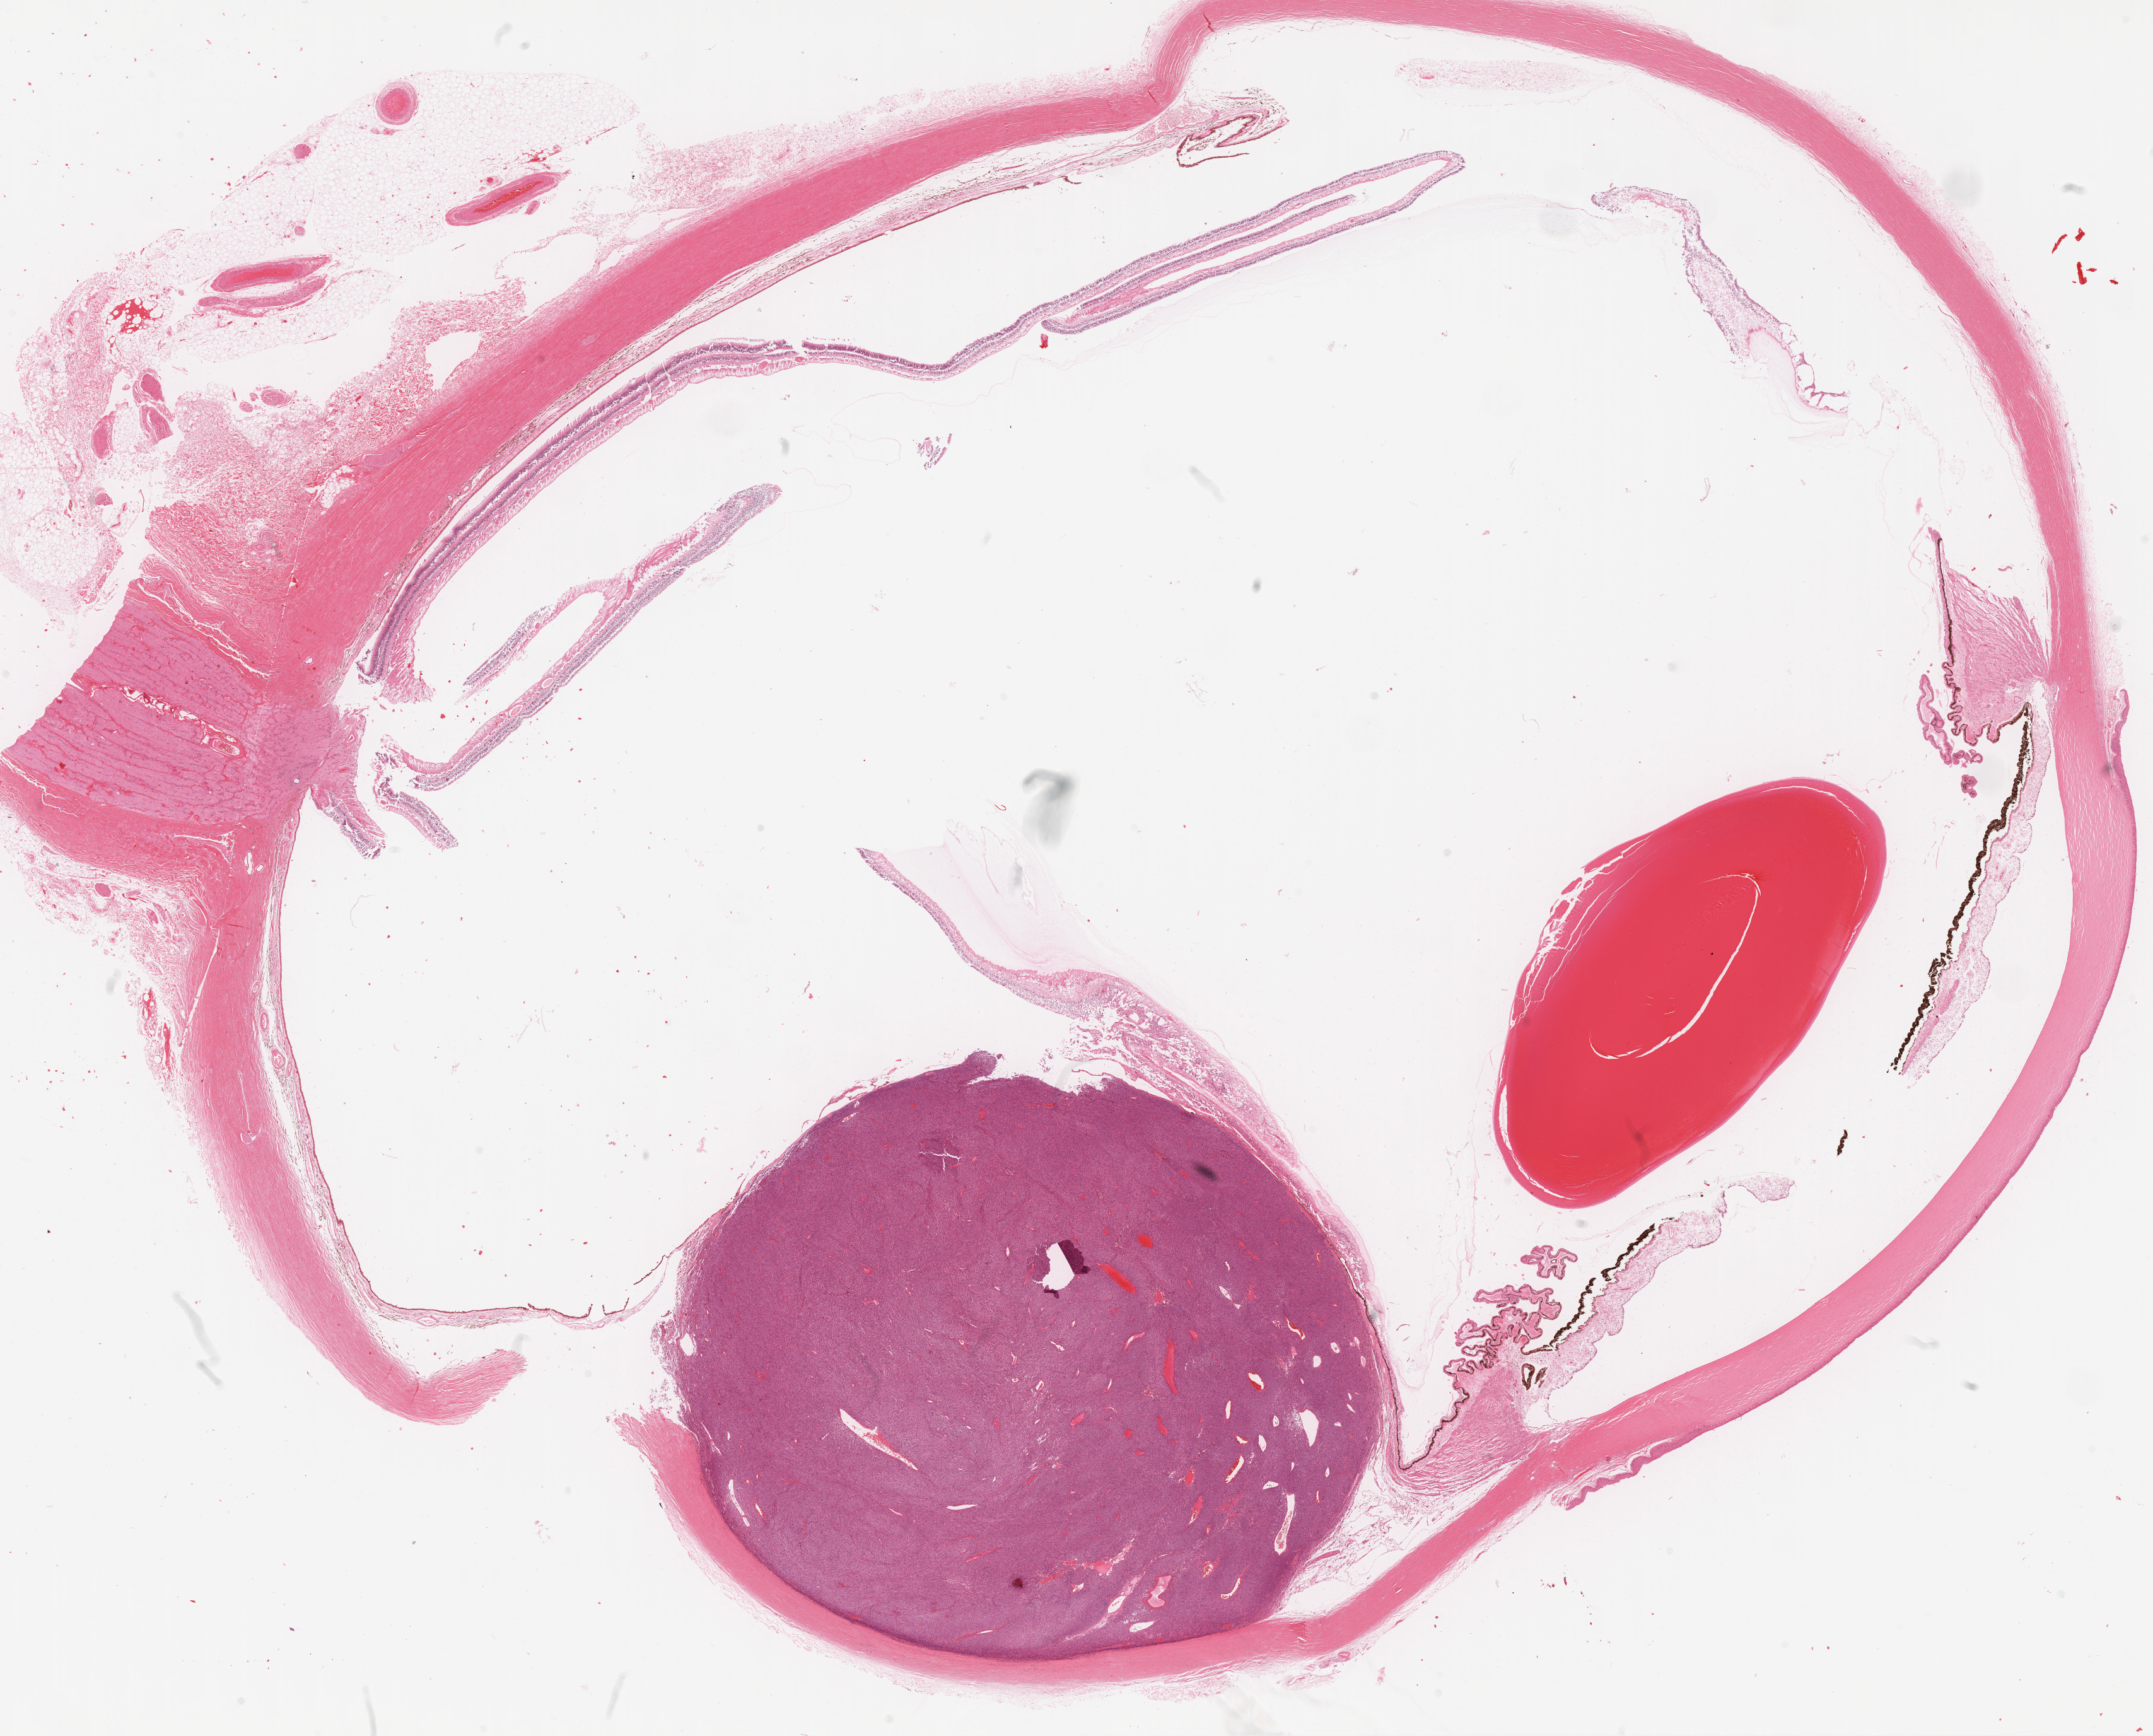
Whole-slide histology image, H&E — low-resolution overview of the scanned area, about 27.5 x 22.2 mm (slide scanned at 20x), formalin-fixed paraffin-embedded (FFPE) diagnostic section, uvea, primary tumour sample. Patient: male, age at initial diagnosis 51 years.
TNM: T2a NX MX. Pathologic diagnosis: Spindle cell melanoma, type B. AJCC pathologic stage: IIA (7th edition).